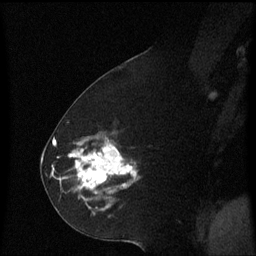
Breast MRI (dynamic contrast-enhanced), one sagittal slice. Slice 30 of 60 in the series (ordered by position). Dynamic contrast-enhanced series, image 2 of 3 at this slice position (ordered by acquisition). 1.5 T. TE 4.2 ms, TR 8.4 ms. 2.2 mm slice thickness. 256 × 256 image matrix. Patient: female, 60 years. From the clinical record (not read from this slice): setting: breast cancer imaged before/during neoadjuvant chemotherapy; receptor status: triple-negative.
Annotated regions visible in this slice (semi-automatic segmentation, software-assisted and operator-edited):
- analysis volume of interest (the breast-tissue region the enhancement analysis was run in; not a lesion): bounding box <69,142,137,215> (left, top, right, bottom; pixels)
- tumour enhancement mask (voxels above the 70 % enhancement threshold inside the analysis volume of interest): <69,142,137,193>